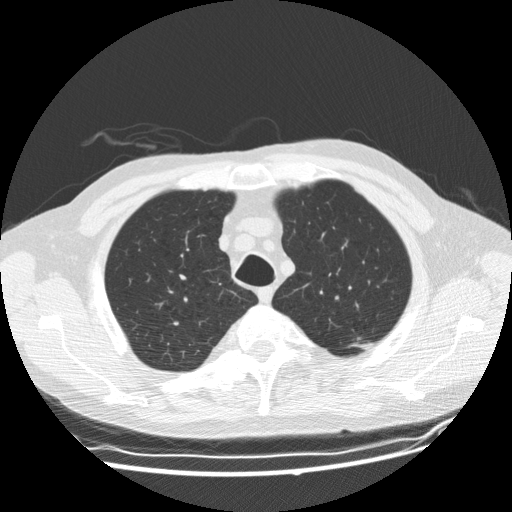
Low-dose screening chest CT, one axial slice. Slice 149 of 177 in the series (ordered by position). Reconstruction kernel STANDARD. 120 kVp. Lung window (W 1500 / L -600 HU). 2.5 mm slice thickness. 512 × 512 image matrix, field of view 360 × 360 mm.
Structures marked on this image (outlined manually by an expert reader):
- lesion 1 (tumor, upper lobe of left lung): box from (x=357, y=336) to (x=362, y=342) px